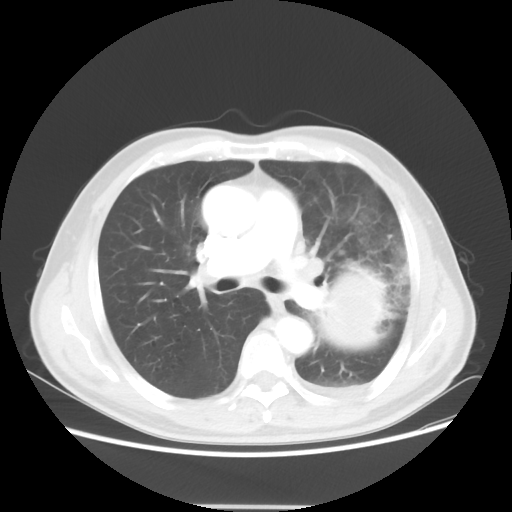
Chest CT, one axial slice. Position 32 of 53 along the scan axis. 100 kVp. Lung window (W 1500 / L -600 HU). 5 mm slice thickness. 512 × 512 image matrix, field of view 391 × 391 mm. Patient: male, 60 years. Case-level facts recorded for this patient, not image findings: clinical TNM (as recorded): T4 N1 M1a.
Outlined on this slice (rectangle marked by the reading radiologist):
- lung tumour (recorded histology: large cell carcinoma): bounding box <305,255,390,346> (left, top, right, bottom; pixels)